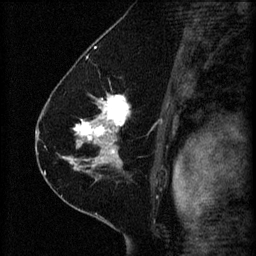
Breast MRI (dynamic contrast-enhanced), one sagittal slice. 3 images stored at this slice position (order not interpretable as contrast timing). 1.5 T. TE 4.2 ms, TR 8.2 ms. 2 mm slice thickness. 256 × 256 image matrix, field of view 180 × 180 mm. Patient: female, 41 years.
Annotated regions visible in this slice (semi-automatic segmentation, software-assisted and operator-edited):
- analysis volume of interest (the breast-tissue region the enhancement analysis was run in; not a lesion): bounding box (x1, y1, x2, y2) in pixels: (67, 94, 165, 173)
- tumour enhancement mask (voxels above the 70 % enhancement threshold inside the analysis volume of interest): (67, 94, 162, 173)